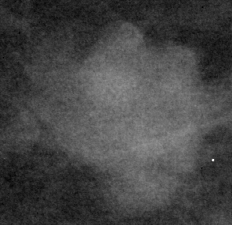
Cropped region of a digitized screen-film mammogram centred on a radiologist-marked abnormality, right breast, CC view, BI-RADS breast density category 1 (scale 1–4).
Finding: mass, shape lobulated, margins circumscribed / ill defined; BI-RADS assessment category 4; subtlety rating 5 on a 1 (subtle) to 5 (obvious) scale; pathology (as recorded): benign.